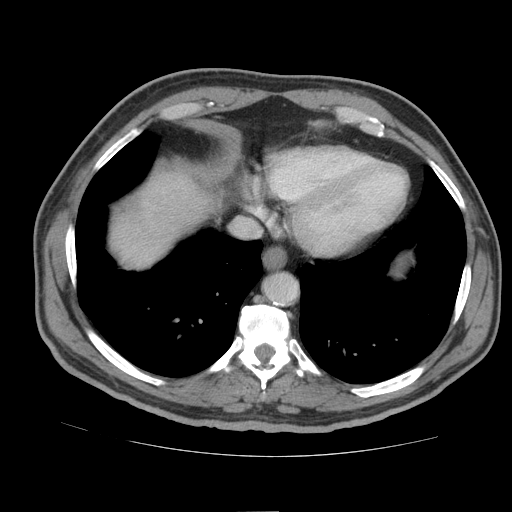
Contrast-enhanced abdominal CT (liver protocol), one axial slice; slice 80 of 105 in the series (ordered by position); reconstruction kernel STANDARD; soft-tissue window (W 400 / L 40 HU); 2.5 mm slice thickness; 512 × 512 image matrix, field of view 380 × 380 mm. Case-level facts recorded for this patient, not image findings: diagnosis: hepatocellular carcinoma (patient treated with transarterial chemoembolisation; whether this scan precedes or follows treatment is not stated here); TNM stage (as recorded): Stage-IIIB; Child-Pugh class: A.
Annotated regions visible in this slice (semi-automatically segmented with operator editing):
- liver parenchyma outside the tumour (the mass and vessels are separate outlines, so this box may not span the whole liver): box from (x=112, y=172) to (x=212, y=266) px